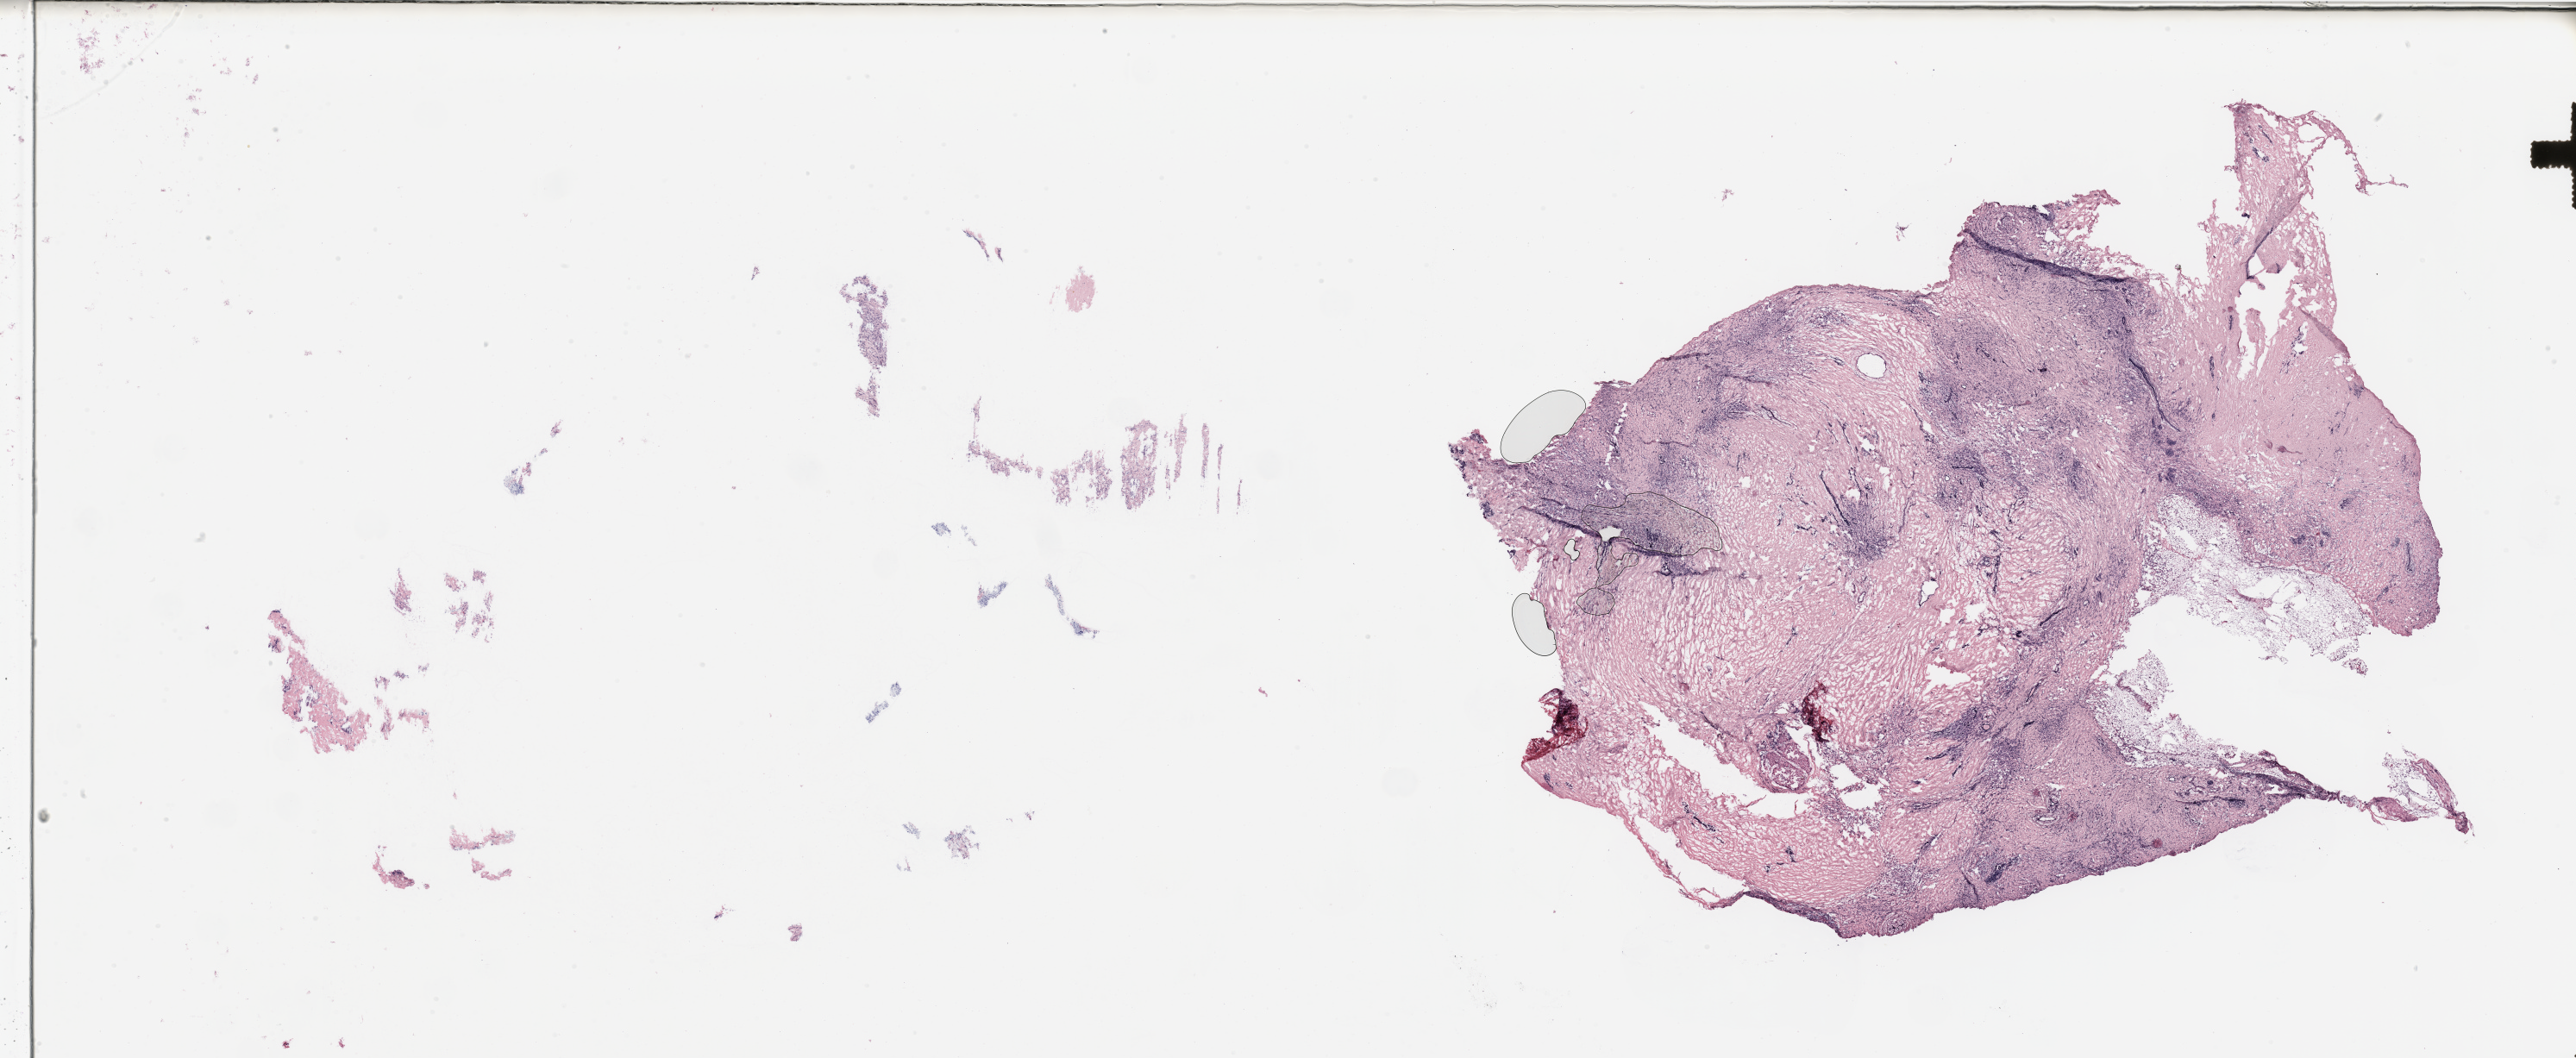
H&E-stained whole-slide image — shown as a low-resolution overview of the whole scanned area (about 47.3 x 19.4 mm, acquisition: 20x scan). Breast, tissue type not recorded.
Patient diagnosis (cohort enrolment): breast cancer (breast).